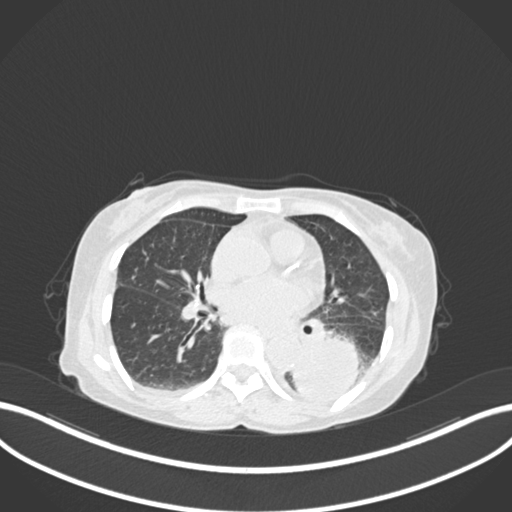
Chest CT, one axial slice. Position 71 of 233 along the scan axis. Reconstruction kernel B30f. 120 kVp. Lung window (W 1500 / L -600 HU). 1 mm slice thickness. 512 × 512 image matrix, field of view 400 × 400 mm. Female patient, age 78 years. From the clinical record (not read from this slice): clinical TNM (as recorded): T3 N0 M1.
Outlined on this slice (bounding box drawn by a radiologist):
- lung tumour (recorded histology: squamous cell carcinoma): box from (x=287, y=332) to (x=362, y=404) px